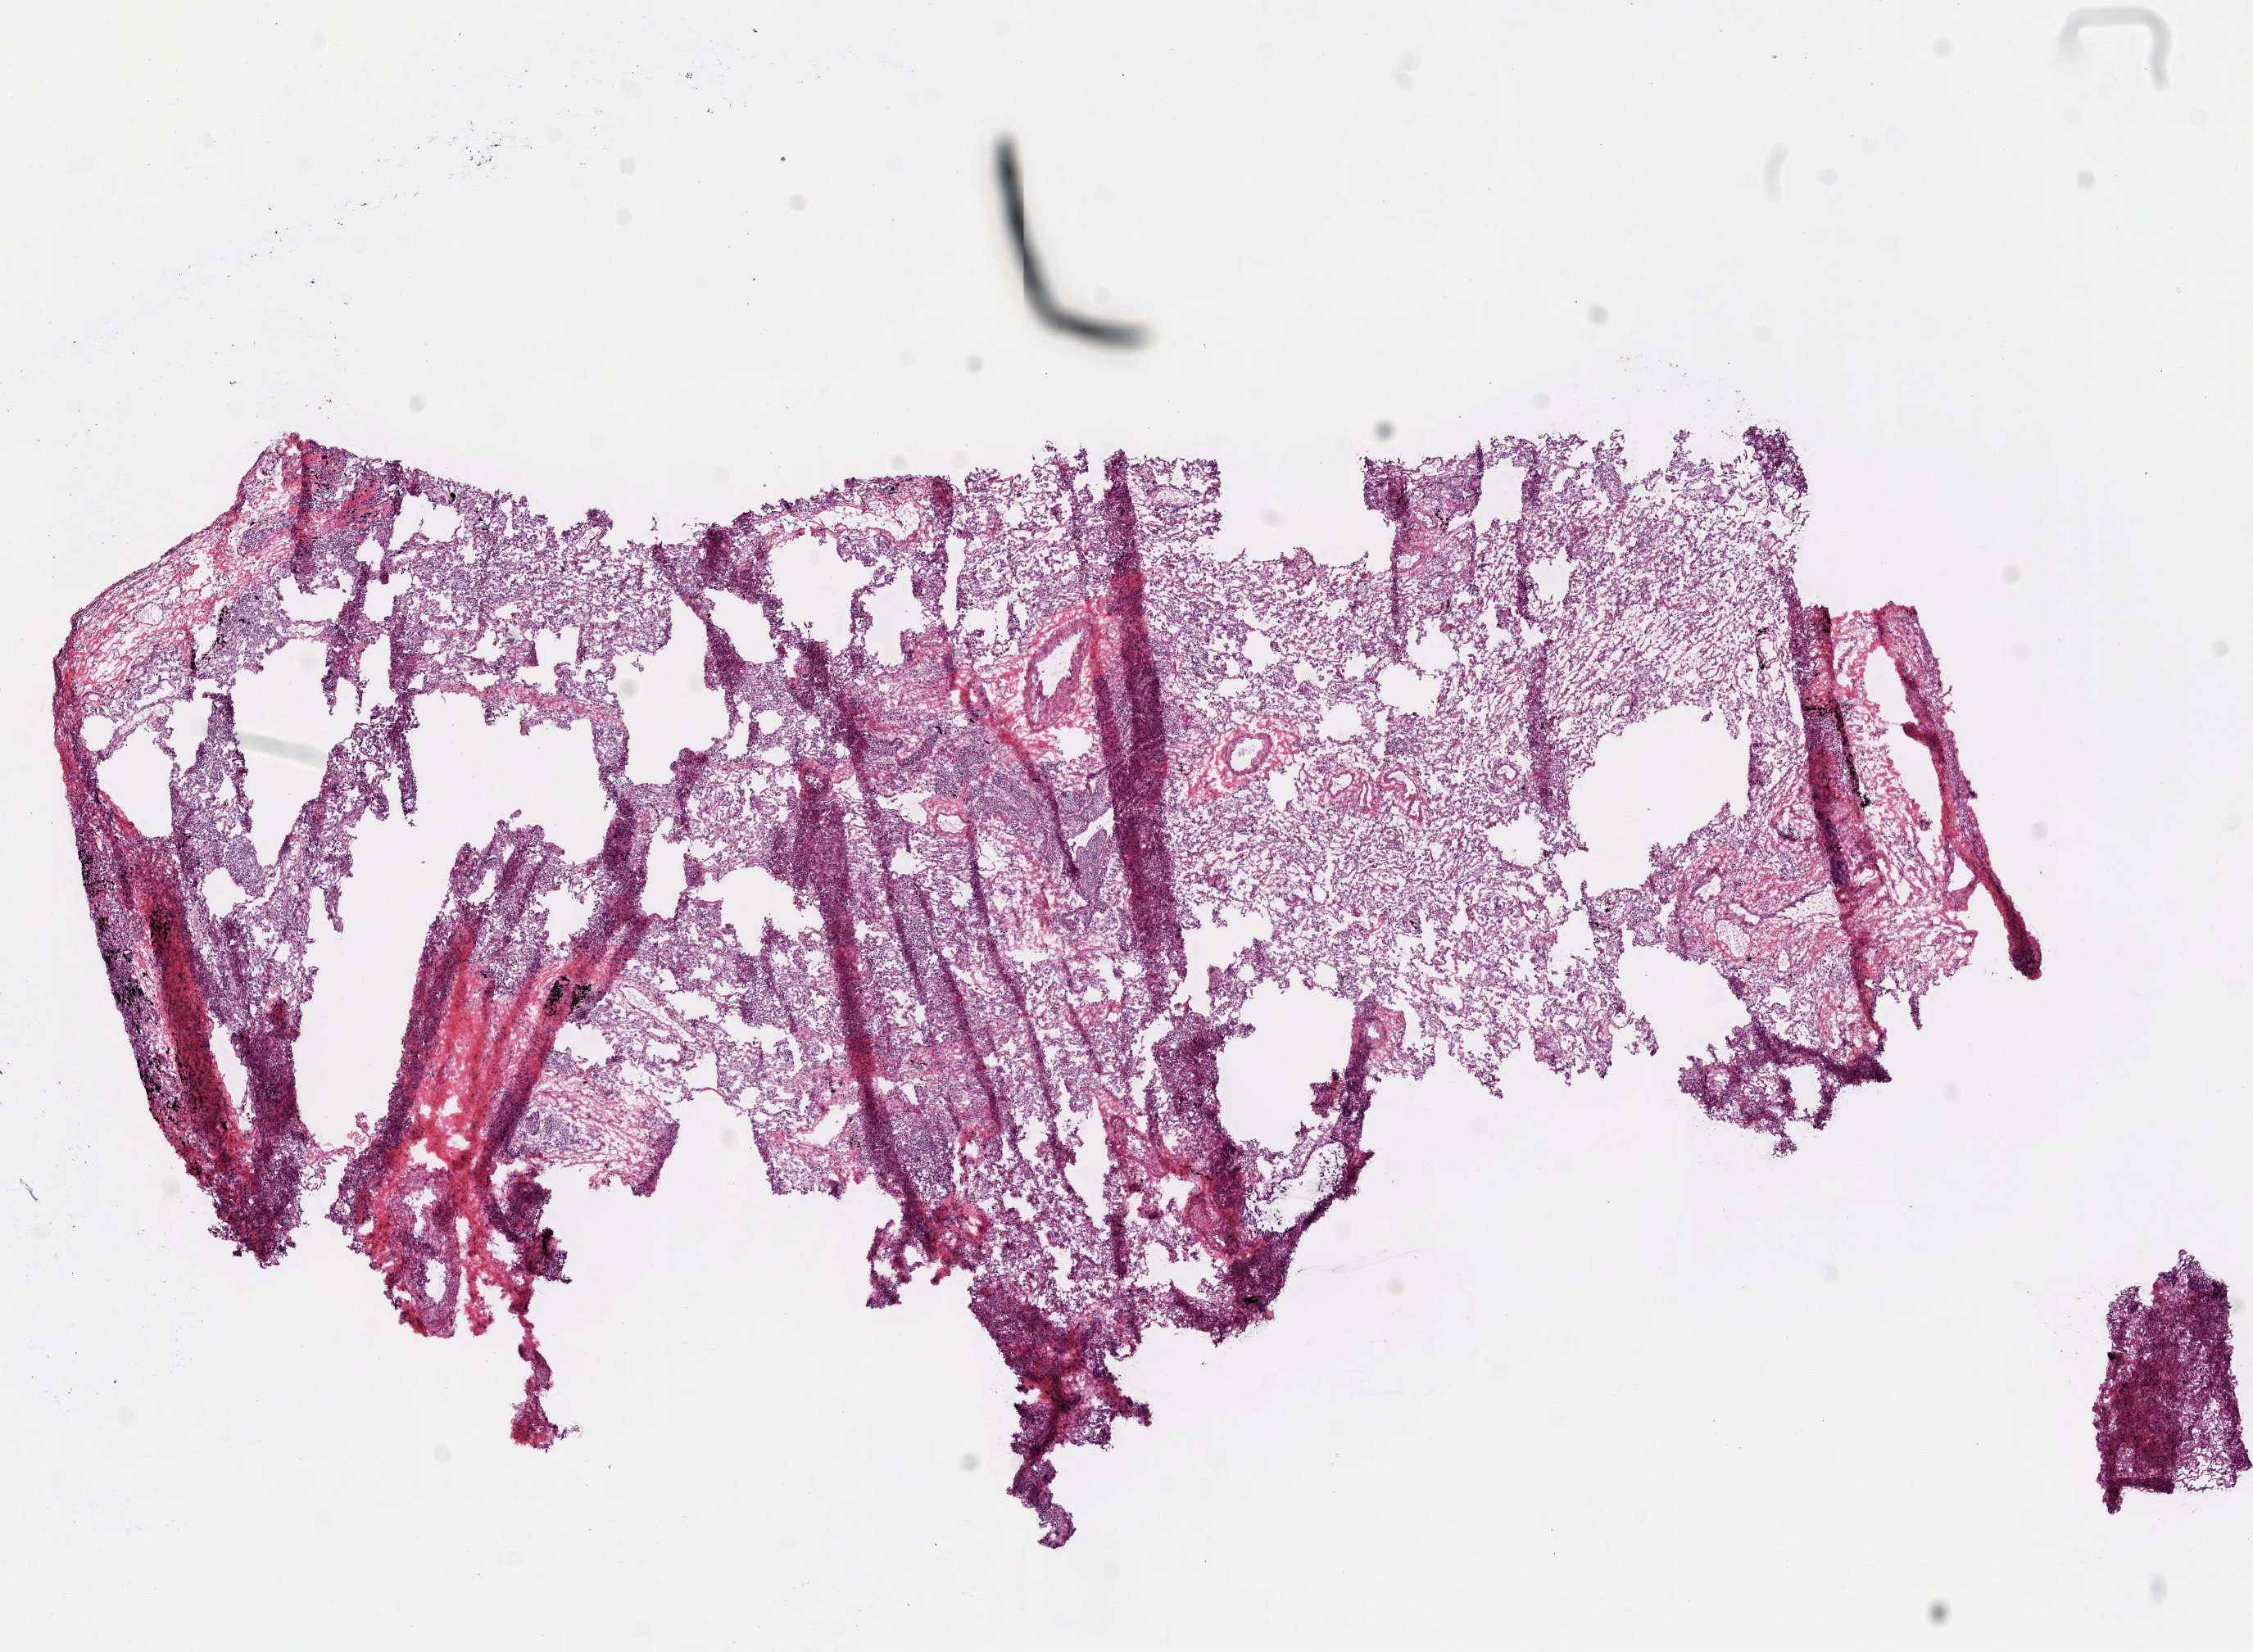
Digitized H&E tissue section (whole slide), shown as a low-resolution overview of the whole scanned area (about 11.0 x 8.1 mm, from a 20x scan). Frozen section from the top of the tissue portion. Lung, solid tissue normal (non-tumour tissue) sample. Male patient; age at initial diagnosis 63 years.
- this section: solid tissue normal sample (biorepository sample class)
- patient diagnosis: Squamous cell carcinoma, NOS (upper lobe, lung)